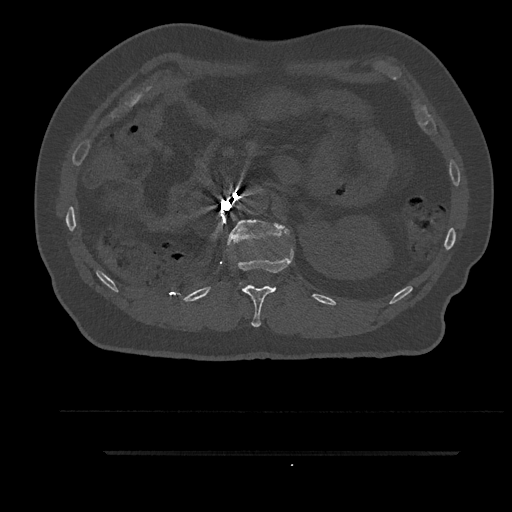
CT including the spine, one axial slice; slice 218 of 797 in the series (ordered by position); reconstruction kernel Br40s/3; bone window (W 1800 / L 400 HU); 0.5 mm slice thickness; 512 × 512 image matrix, field of view 432 × 432 mm. Male patient, age 63 years. Case-level facts recorded for this patient, not image findings: primary cancer: renal.
Annotated regions visible in this slice (semi-automatic segmentation, software-assisted and operator-edited):
- L1 vertebra: bounding box <227,219,289,284> (left, top, right, bottom; pixels)
- T12 vertebra: <232,248,294,327>